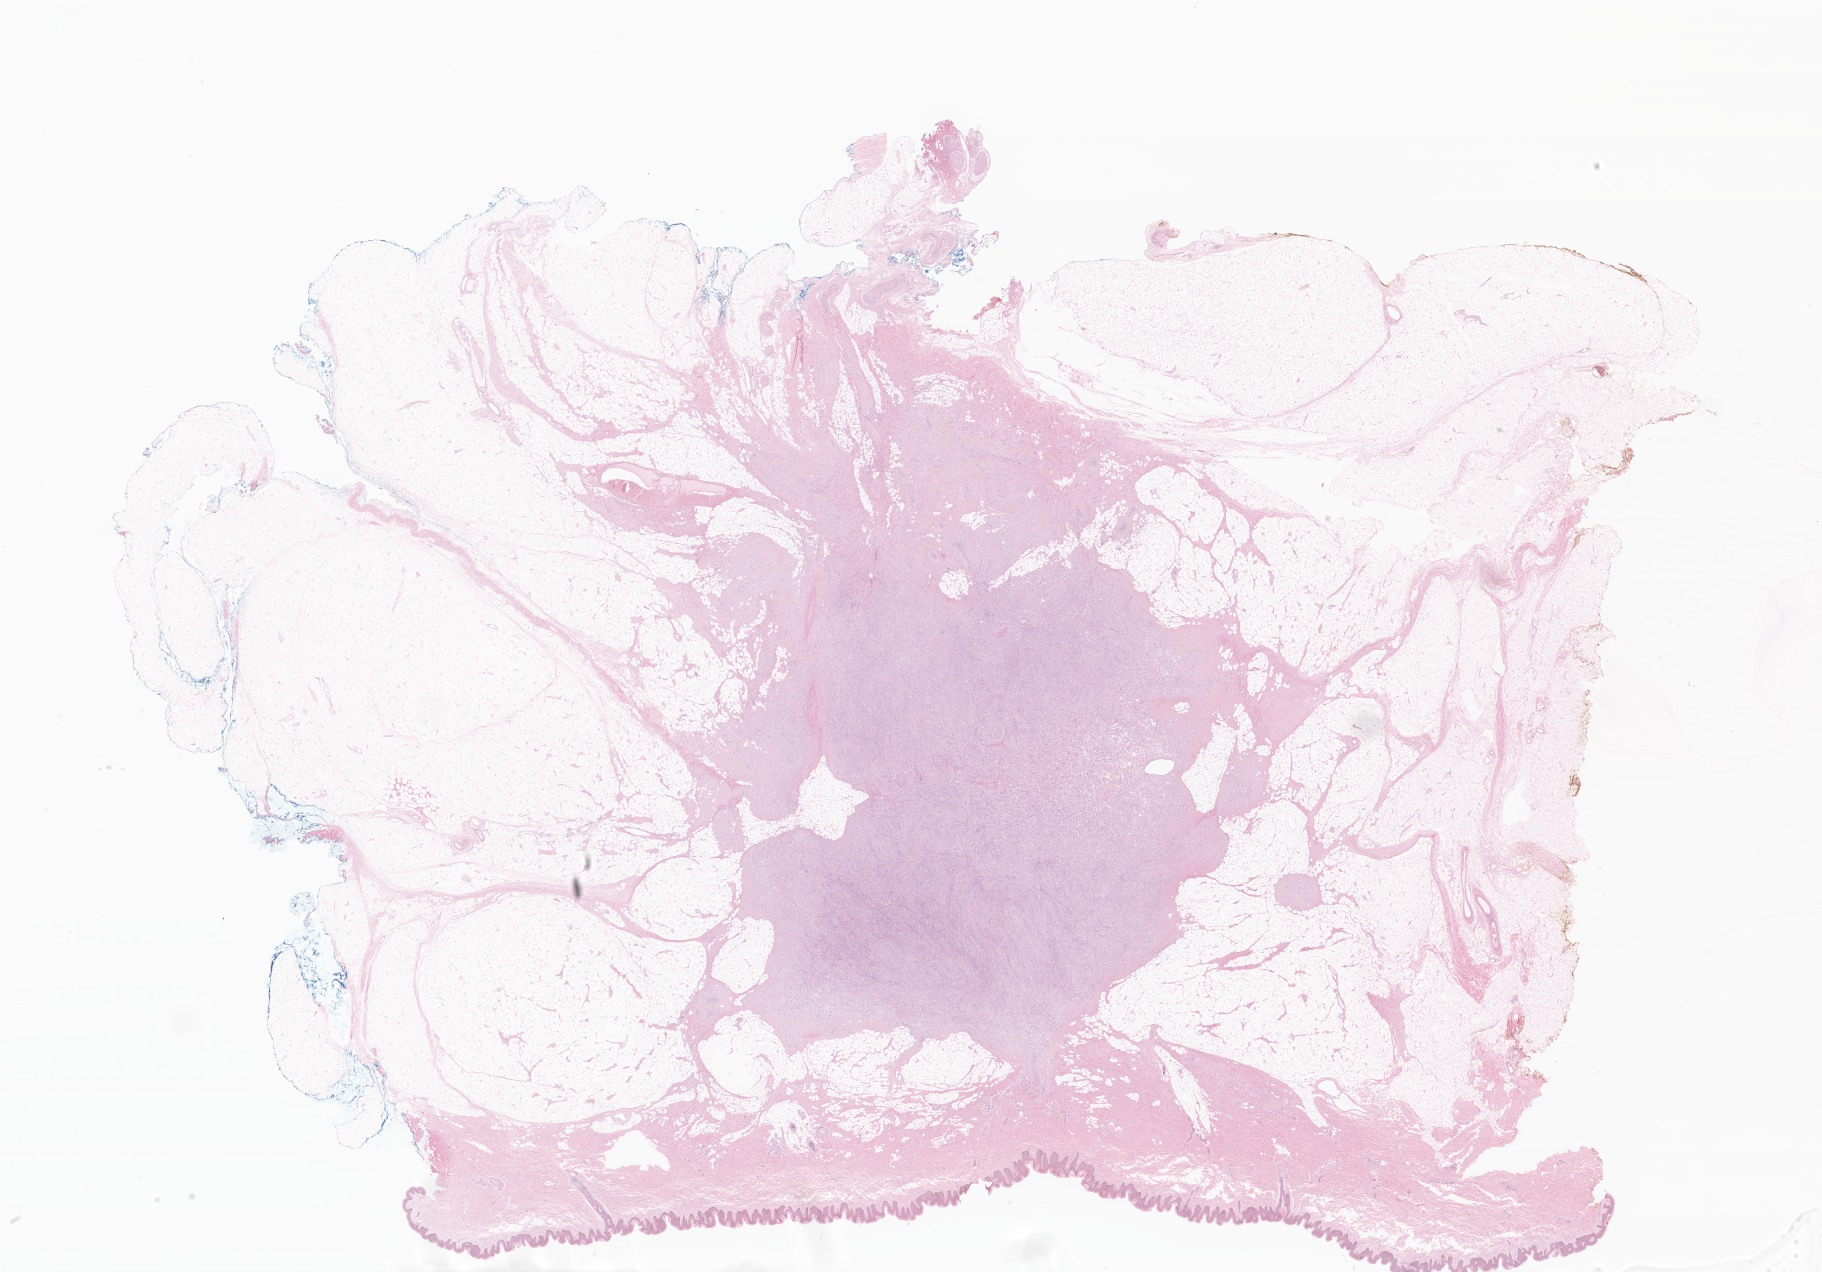
Digitized hematoxylin and eosin (H&E)-stained section of tumor tissue from the skin of lower limb — whole scanned area (about 30.7 x 21.5 mm) shown as a low-resolution overview. FFPE section. Patient: male, age 52 months (4 years 4 months).
* diagnosis (ICD-O-3 morphology term): Plexiform fibrohistiocytic tumor